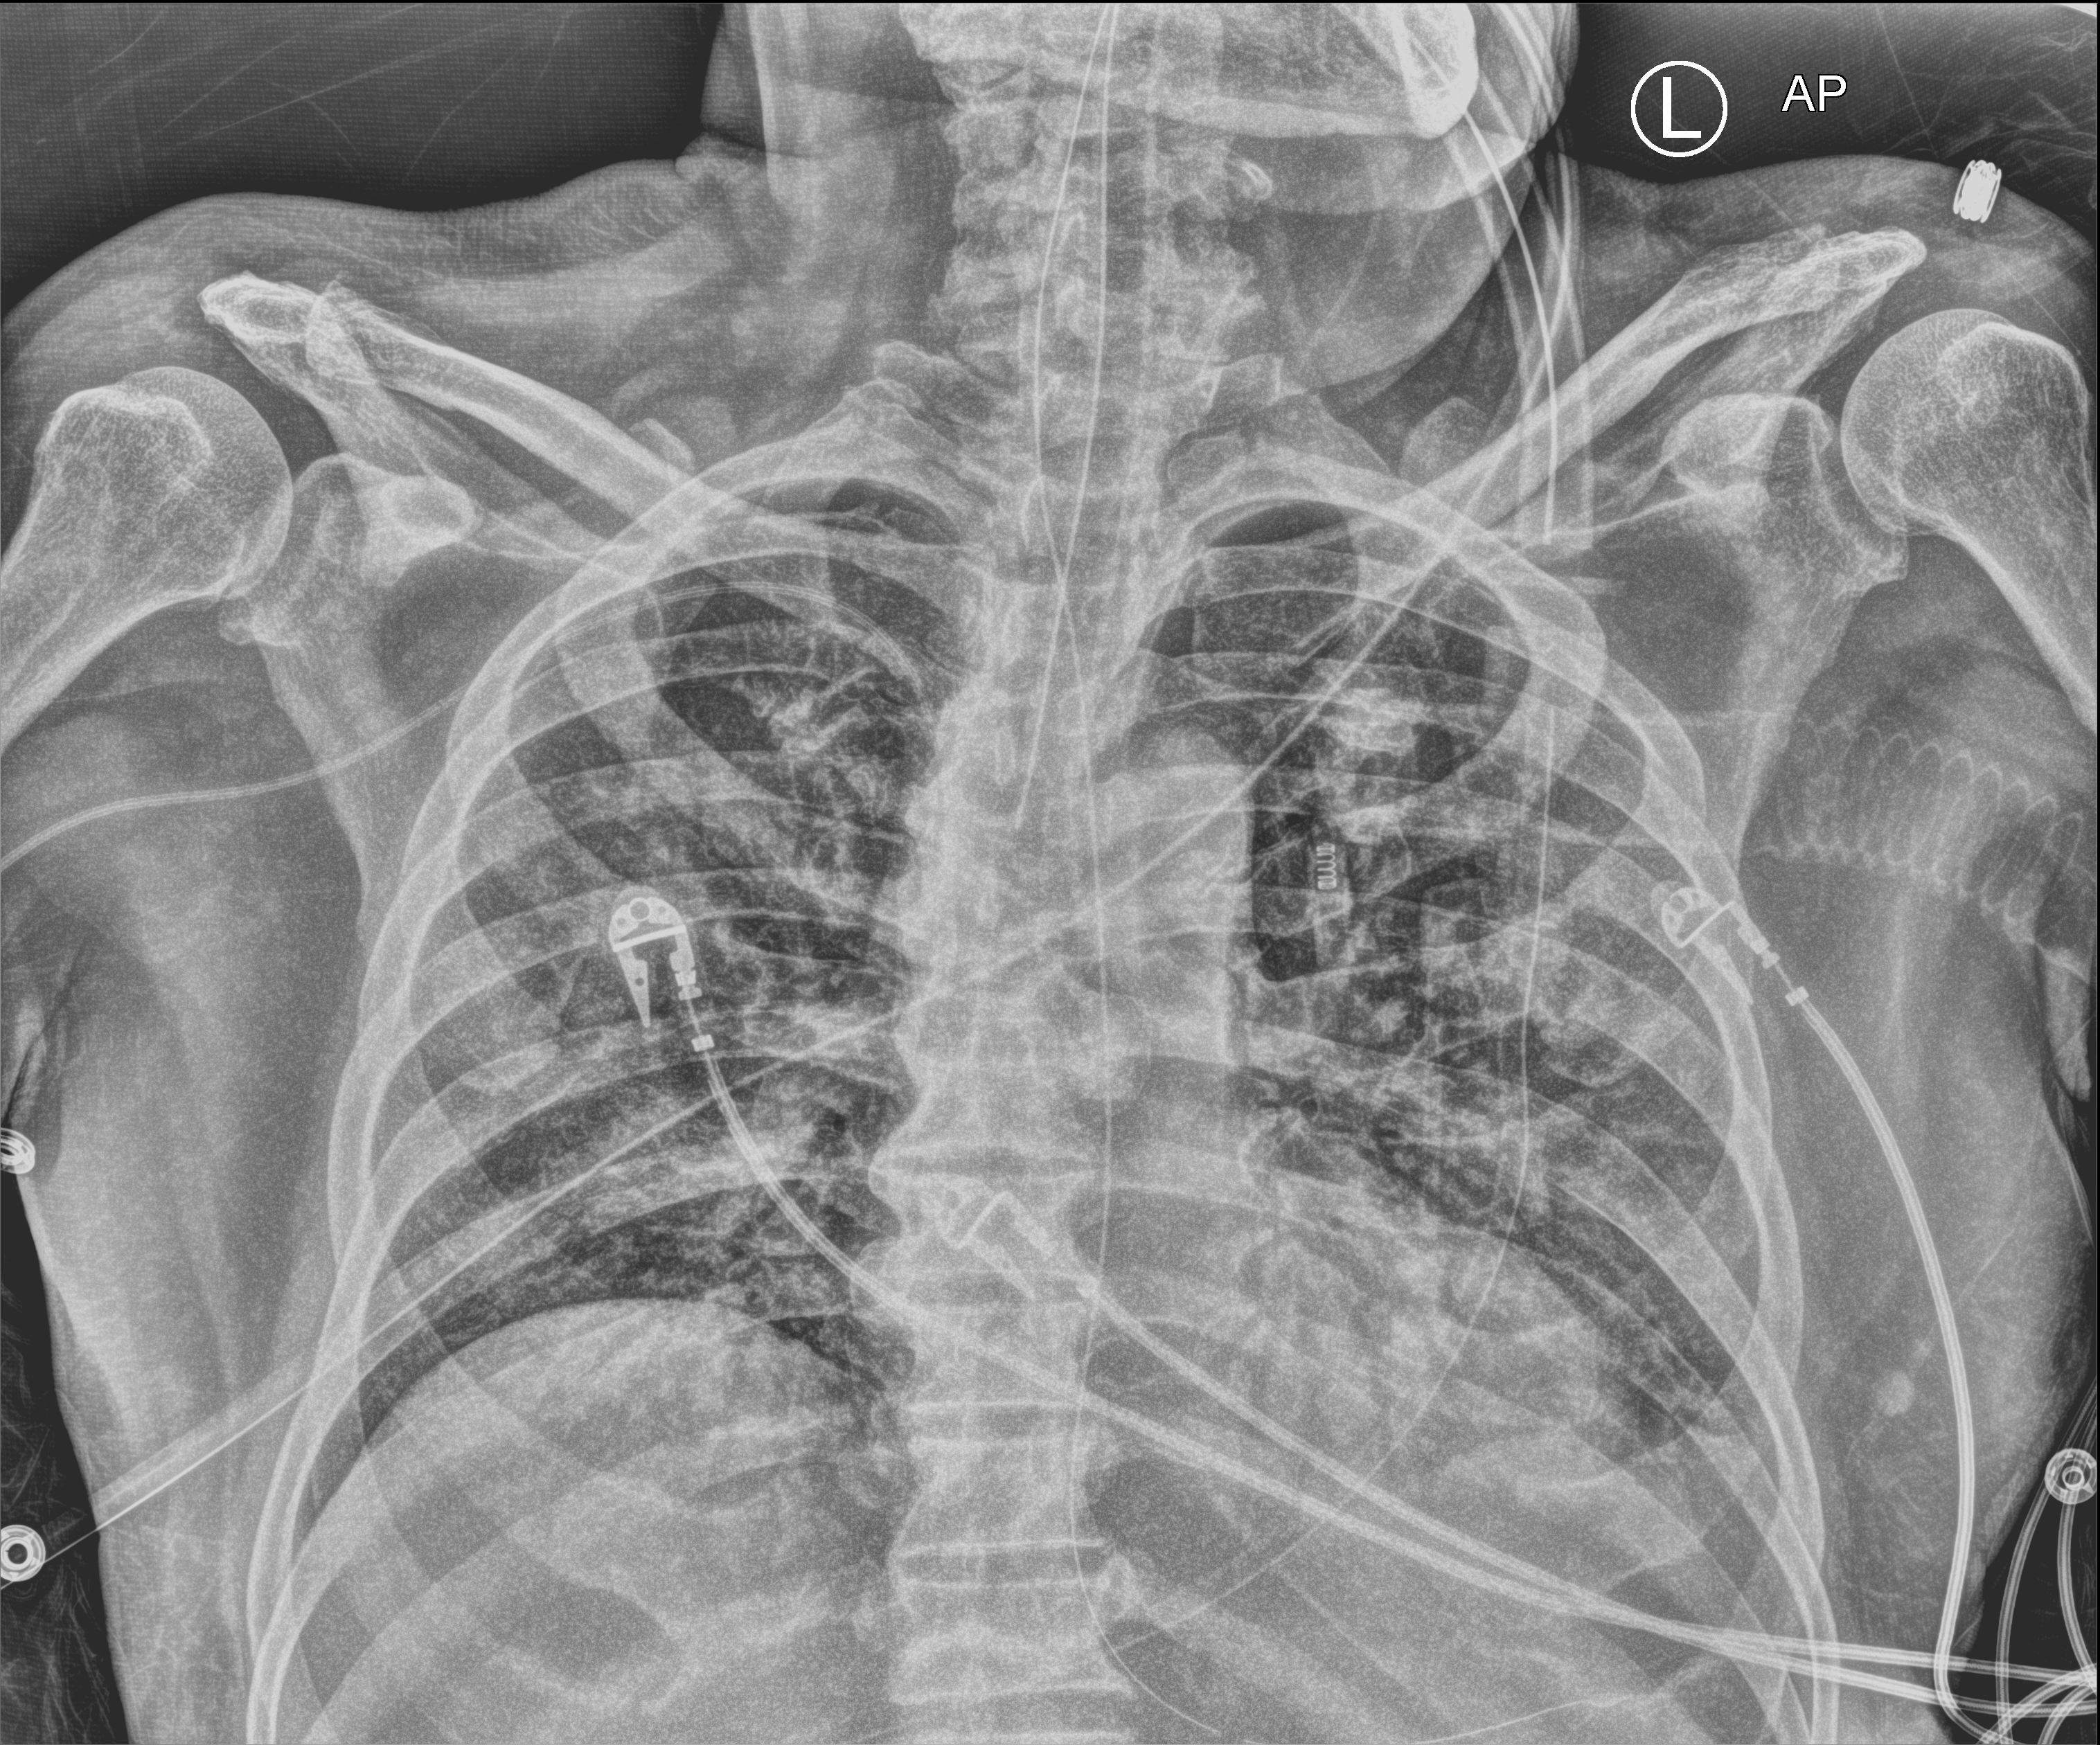
Chest X-ray (portable); anteroposterior (AP) projection. Male patient hospitalised with COVID-19, age 75–90 years.
From the hospital-stay record, not from the radiograph (when in the stay this image was taken is not recorded): mechanically ventilated during this hospital stay: yes.